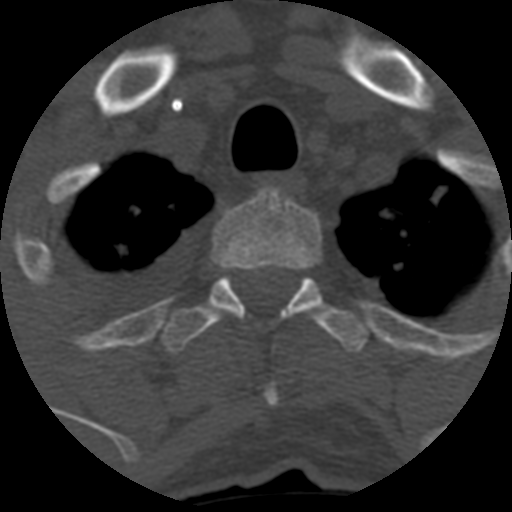
CT including the spine, one axial slice; position 496 of 708 along the scan axis; reconstruction kernel STANDARD; 120 kVp; one of 3 acquisitions stored at this slice position; bone window (W 1800 / L 400 HU); 512 × 512 image matrix, field of view 160 × 160 mm. Patient age 55 years. Case-level facts recorded for this patient, not image findings: primary cancer: colon.
Outlined on this slice (semi-automatically segmented with operator editing):
- T2 vertebra: bounding box <212,190,322,404> (left, top, right, bottom; pixels)
- T3 vertebra: <161,274,368,353>